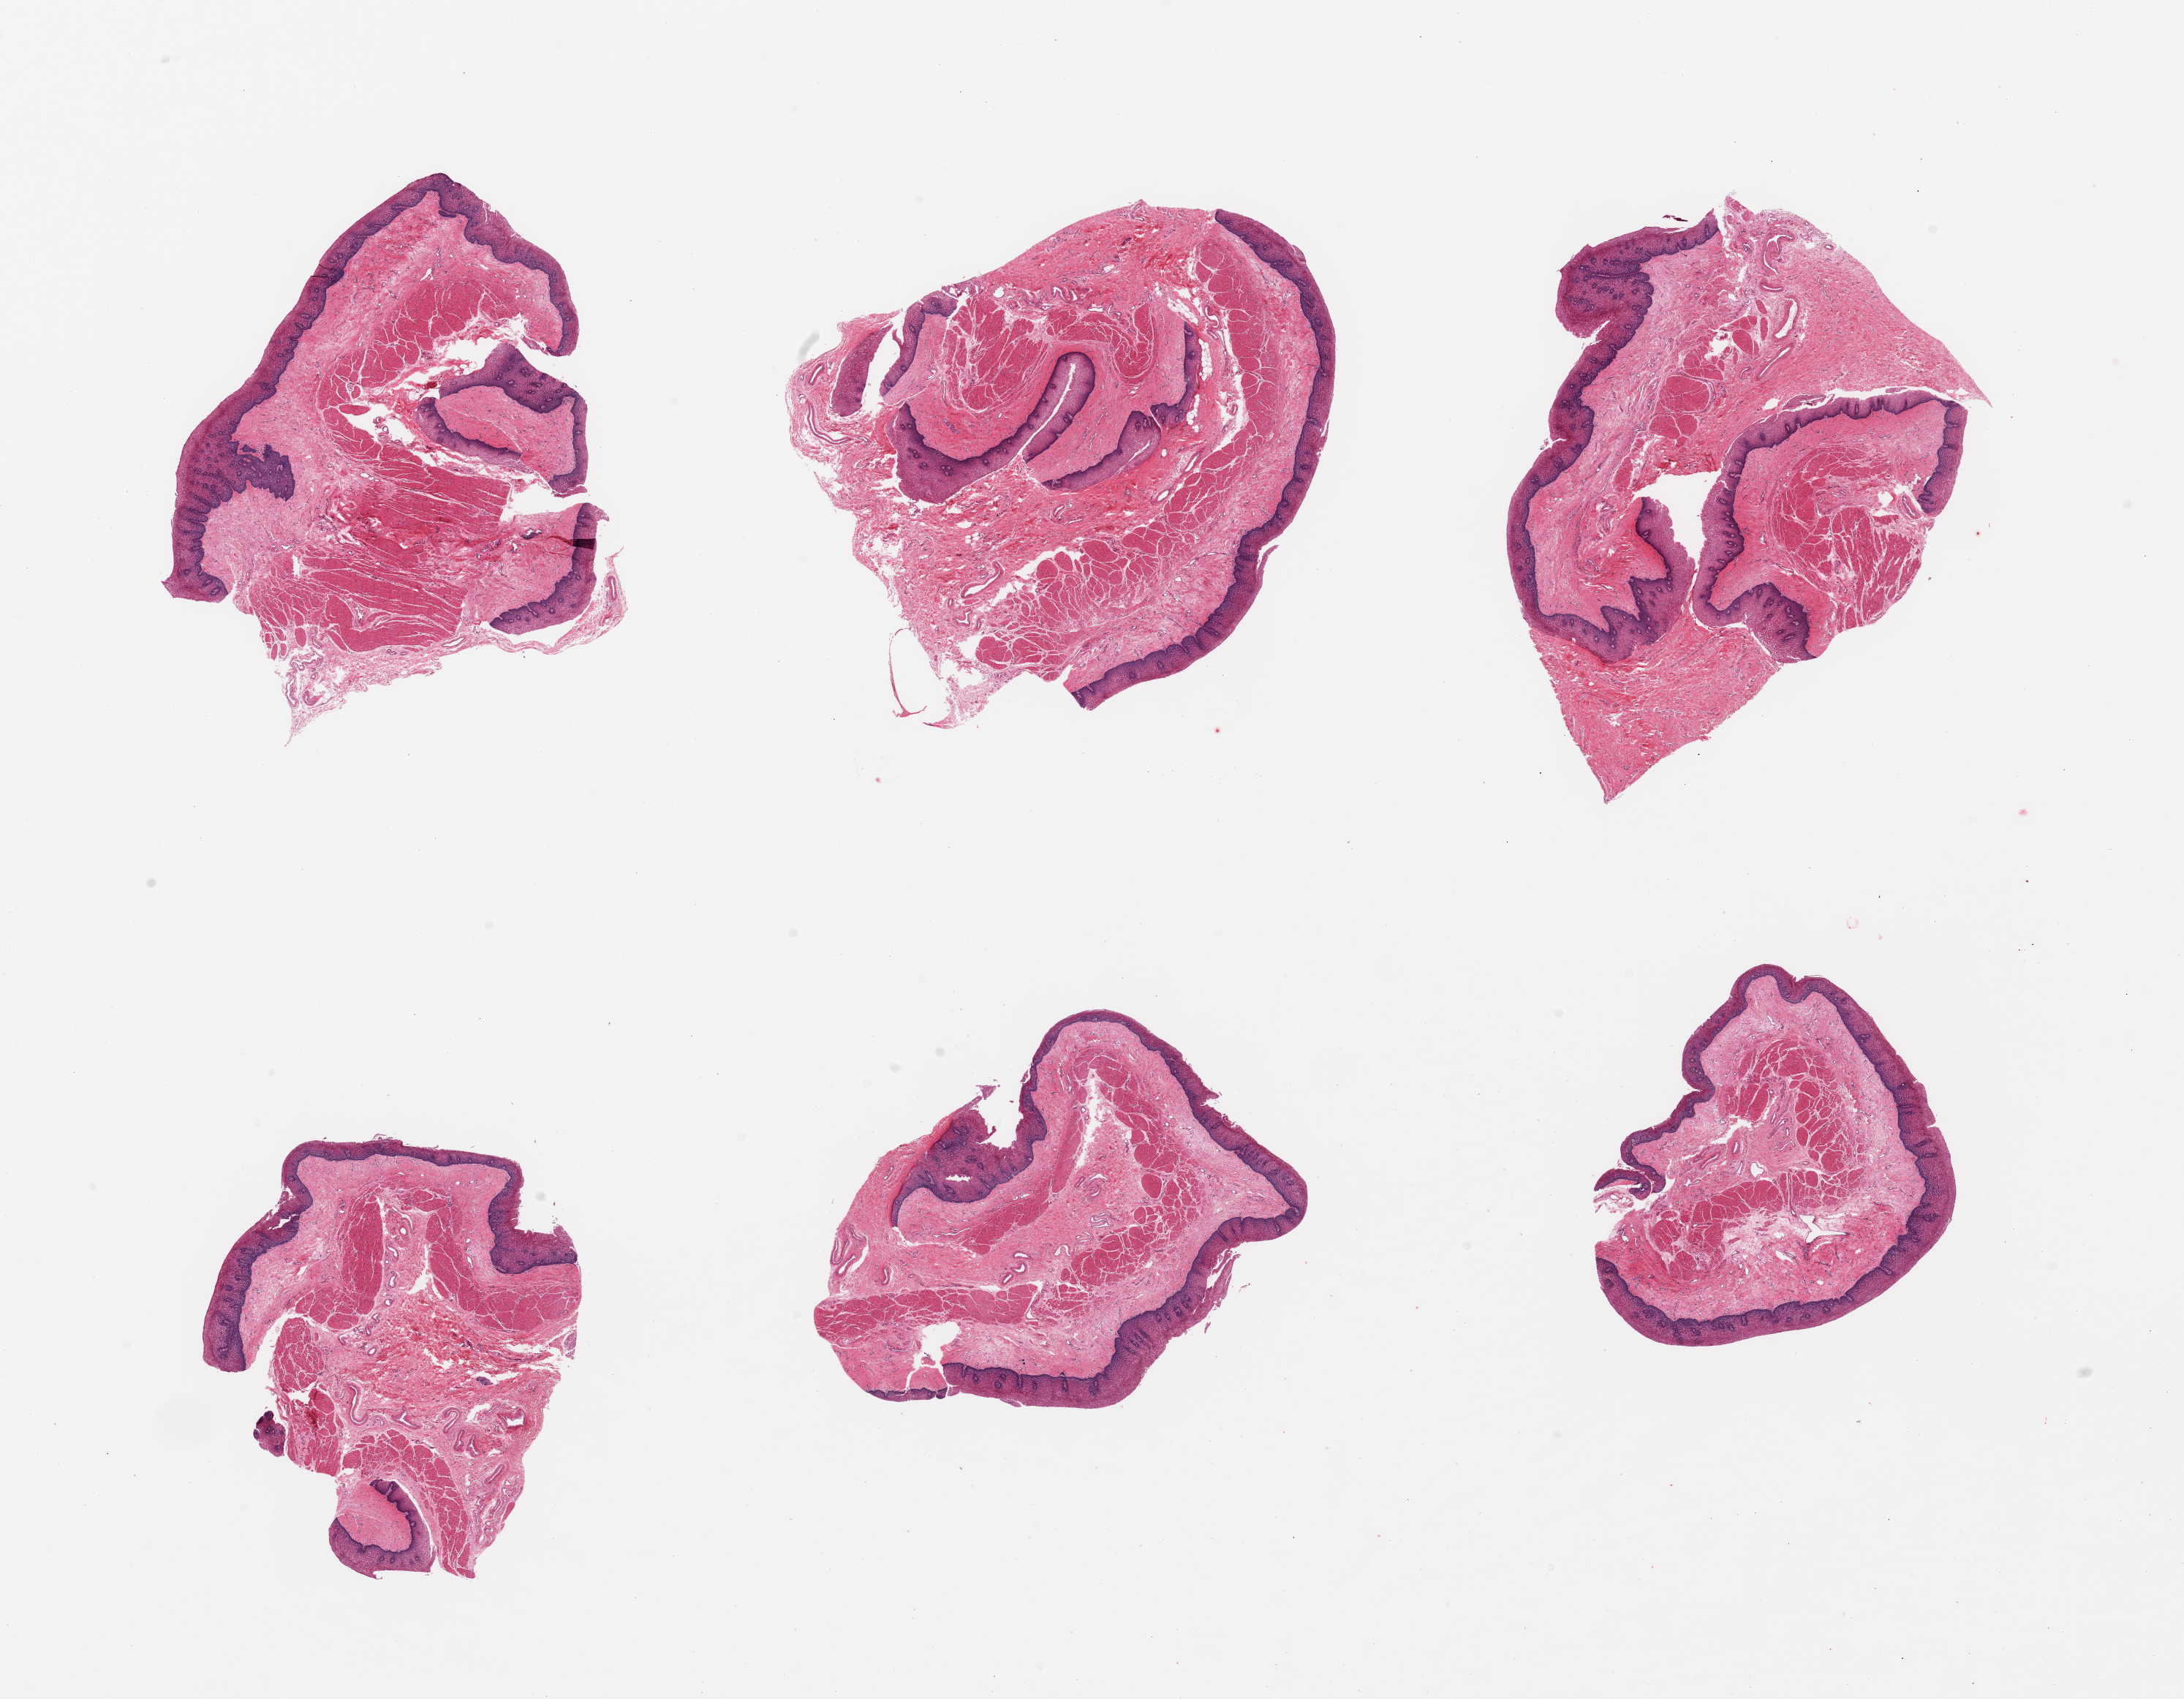
Hematoxylin and eosin (H&E) whole-slide image — a low-resolution overview of the entire scanned area, about 23.6 x 18.4 mm (acquisition: 20x scan); PAXgene-fixed paraffin-embedded (PFPE) section; sampled site (target tissue): esophageal muscle; donor tissue sample. Donor: male.
* reviewer comment on this tissue sample: 6 pieces; mucosa, not muscularis